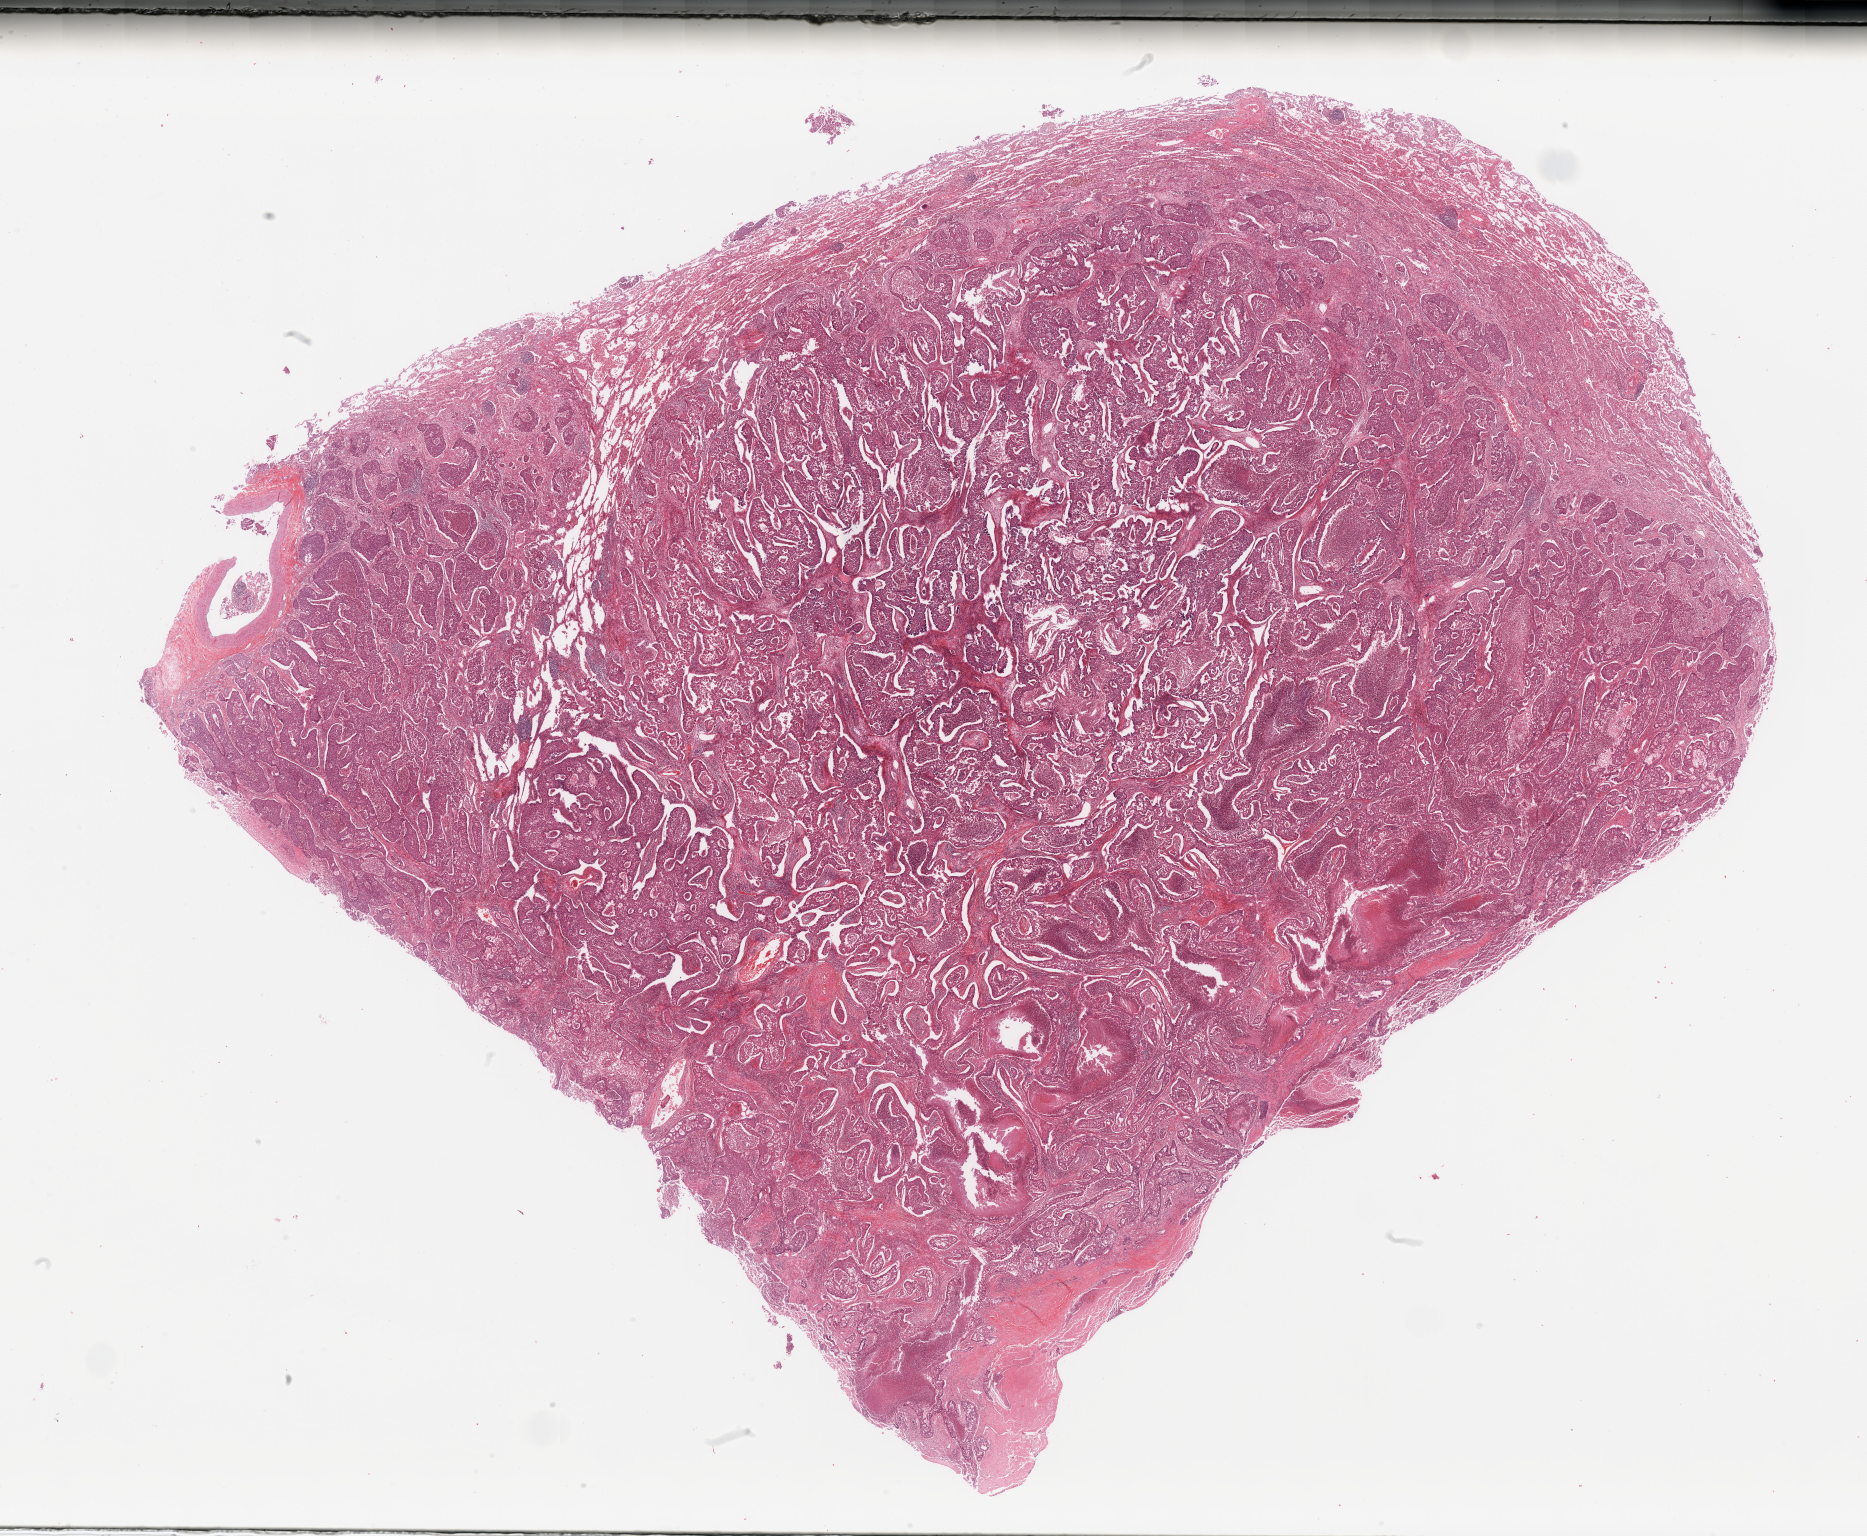
Whole-slide histology image, H&E, a low-resolution overview of the entire scanned area, about 29.5 x 24.3 mm; lung, tumour tissue. Patient: male, age 58 years. Histologic grade: G3 (poorly differentiated).
AJCC pathologic stage: IIIA. Diagnosis: Adenocarcinoma, NOS.